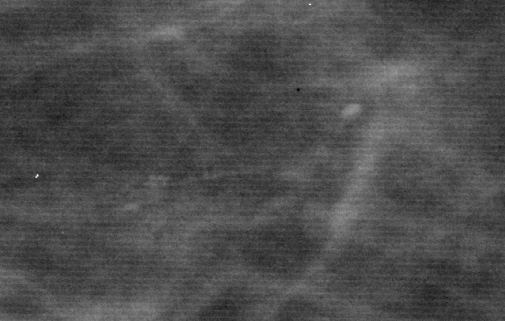
Crop from a digitized film mammogram around one marked abnormality, right breast, CC view, BI-RADS breast density category 2 (scale 1–4).
- Finding: calcifications, morphology fine linear branching, distribution linear; BI-RADS assessment category 4; subtlety rating 2 on a 1 (subtle) to 5 (obvious) scale; pathology (as recorded): benign.